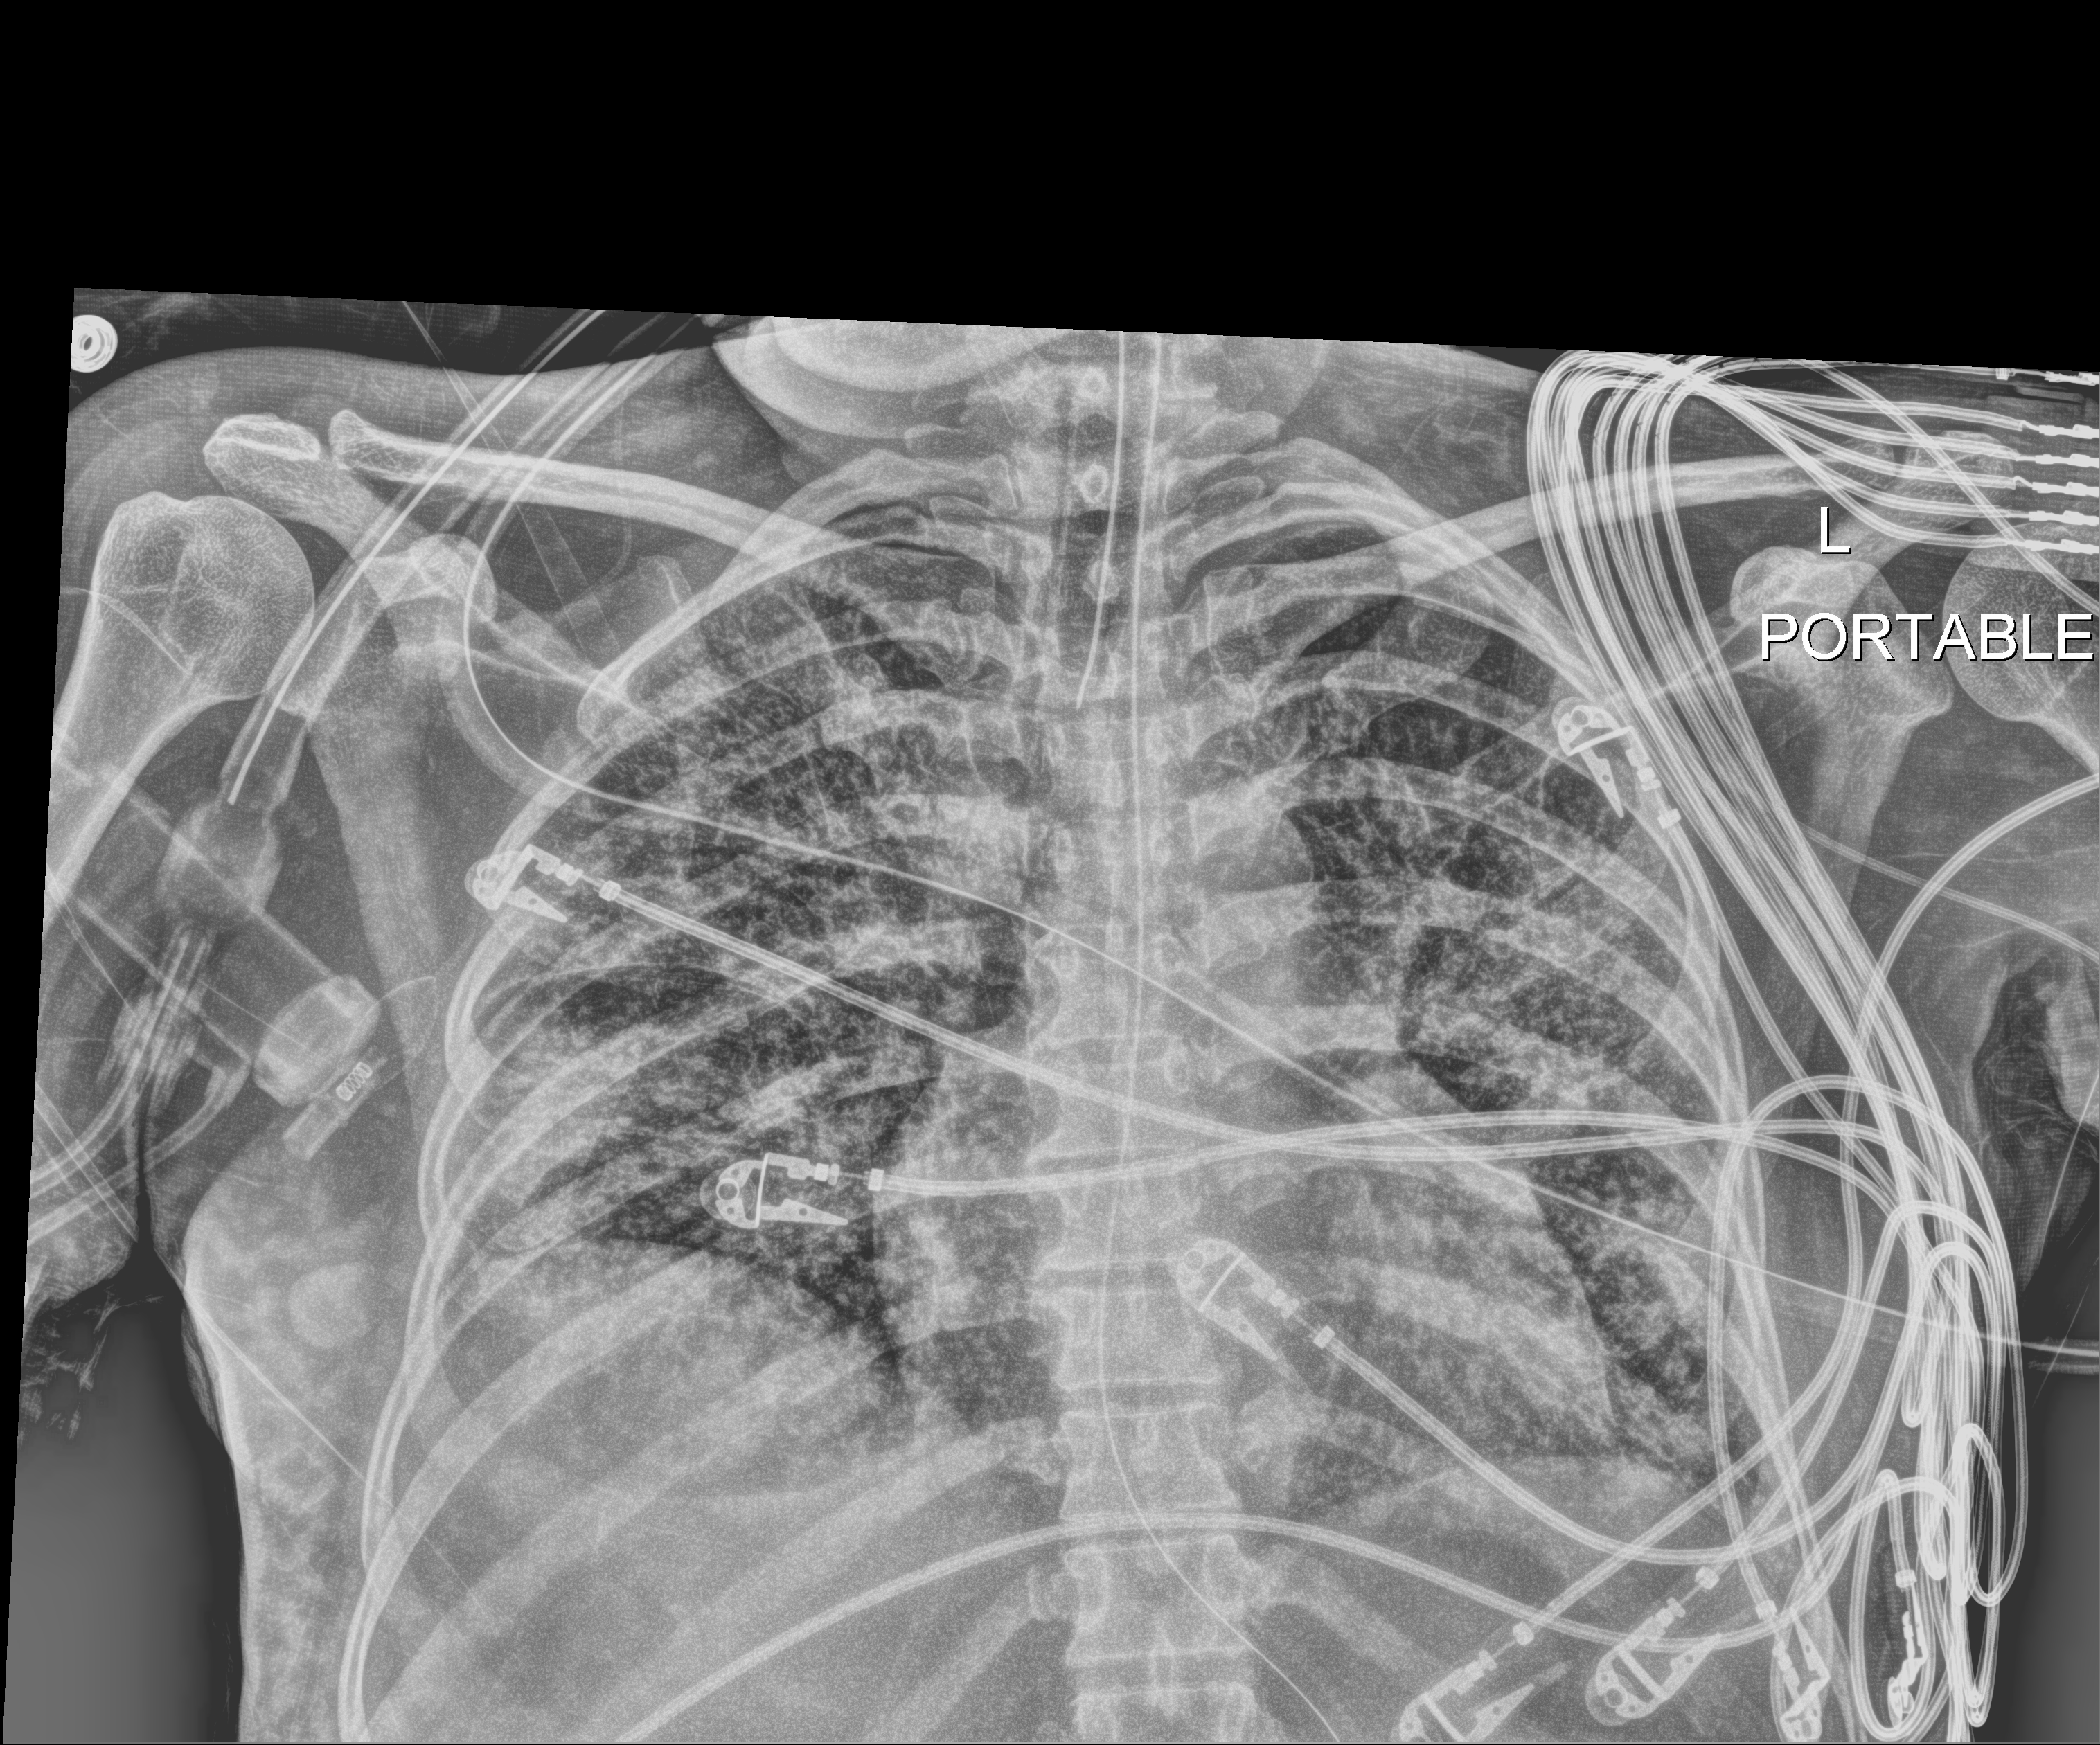
Bedside chest radiograph (digital radiography); anteroposterior (AP) projection. Patient hospitalised with COVID-19; female, aged 18–59 years.
From the hospital-stay record, not from the radiograph (when in the stay this image was taken is not recorded): chronic kidney disease (admission record): no; diabetes (admission record): no; admitted to intensive care during this hospital stay: yes.